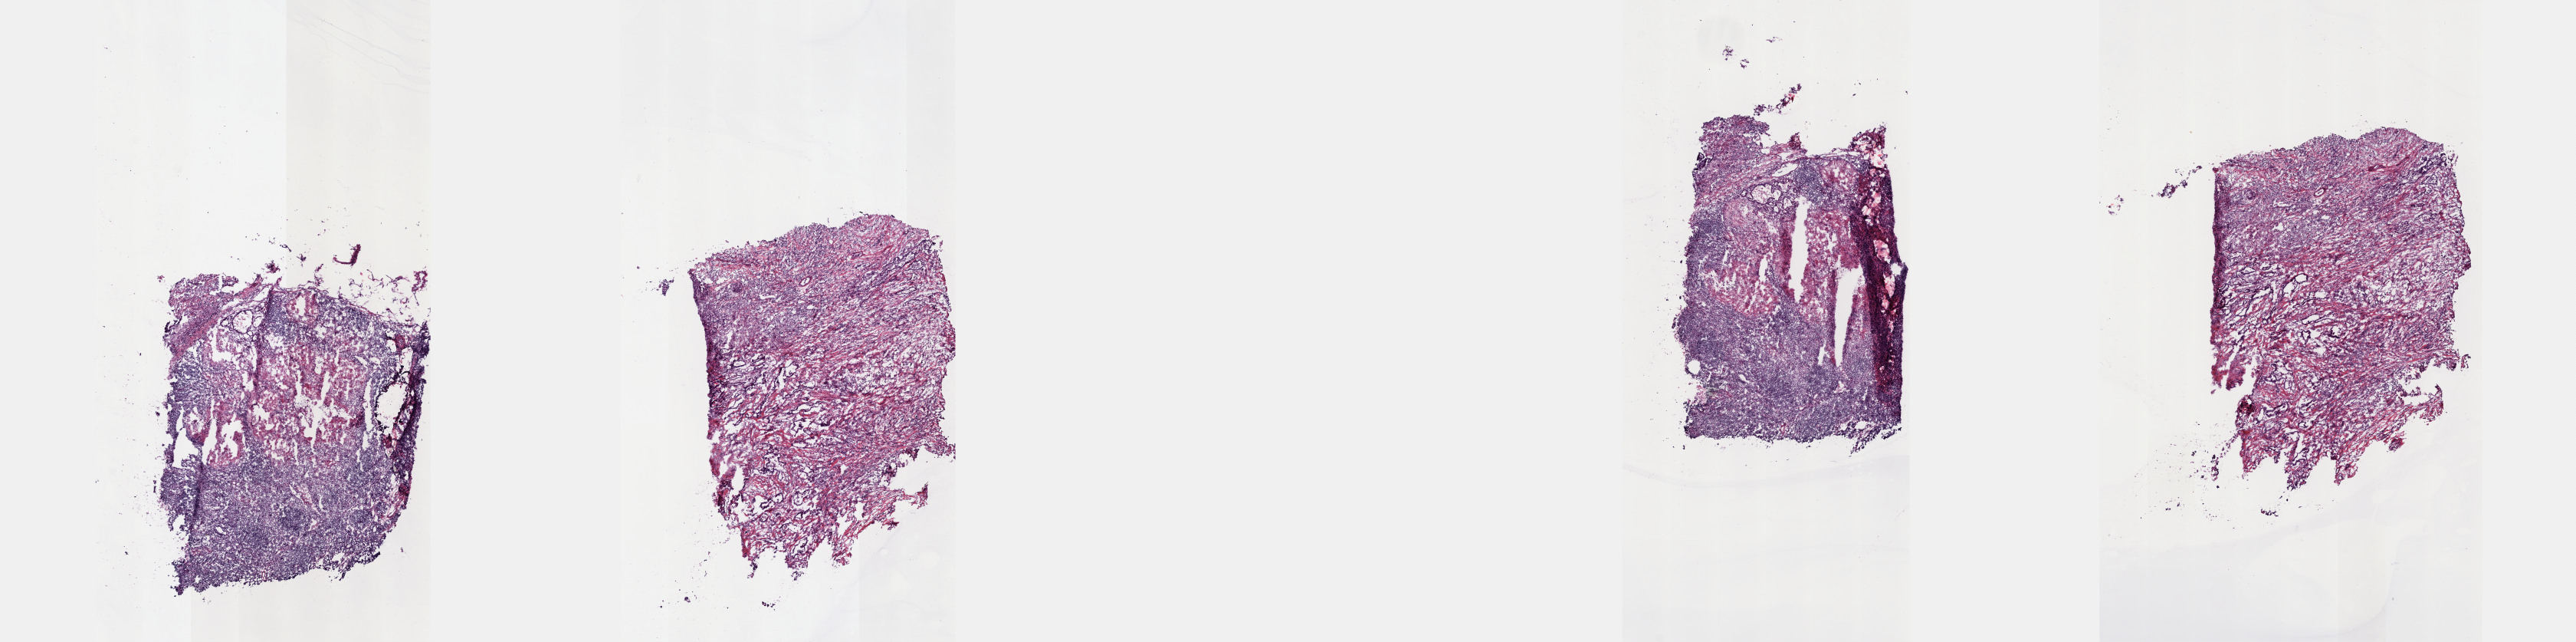
Hematoxylin and eosin (H&E) stained whole-slide image — whole scanned area (about 27.2 x 6.8 mm, from a 40x scan) shown as a low-resolution overview; frozen section; sample: primary tumour, pancreas. Patient: female, age at initial diagnosis 74 years. Histologic grade: G1 (well differentiated). Pathologist review of this section (percent, as recorded): tumour cells 70%, tumour nuclei 70%, normal cells 0%, stromal cells 25%, necrosis 5%. Inflammatory infiltration, as recorded: lymphocyte infiltration 70%, monocyte infiltration 10%, neutrophil infiltration 10%.
AJCC pathologic stage: IIA (7th edition). Pathologic diagnosis: Infiltrating duct carcinoma, NOS. Lymph nodes positive (case pathology): 0 of 9 examined.